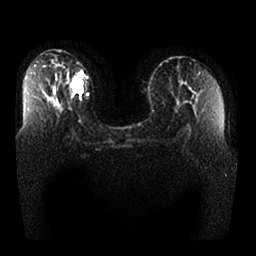
Breast MRI, one axial slice. Slice 15 of 25 in the series (ordered by position). Diffusion-weighted series; image 2 of 4 stored at this slice position (different b-values; order by instance number). 1.5 T. 4 mm slice thickness. 256 × 256 image matrix, field of view 370 × 370 mm. Female patient.
Outlined on this slice (manually delineated by an expert):
- tumour on diffusion-weighted imaging: bounding box <71,77,84,94> (left, top, right, bottom; pixels)